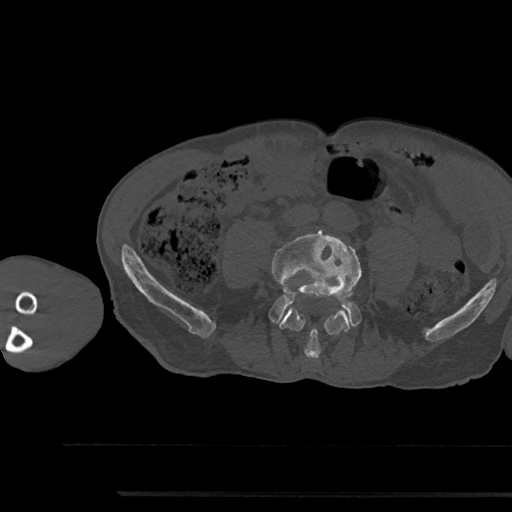
CT including the spine, one axial slice. Reconstruction kernel Br40s/3. Bone window (W 1800 / L 400 HU). 0.5 mm slice thickness. 512 × 512 image matrix, field of view 367 × 367 mm. Patient: male, 79 years. From the clinical record (not read from this slice): primary cancer: prostate.
Annotated regions visible in this slice (semi-automatic segmentation, software-assisted and operator-edited):
- L4 vertebra: bounding box [x1, y1, x2, y2] px = [272, 230, 362, 360]
- L5 vertebra: [270, 295, 360, 326]